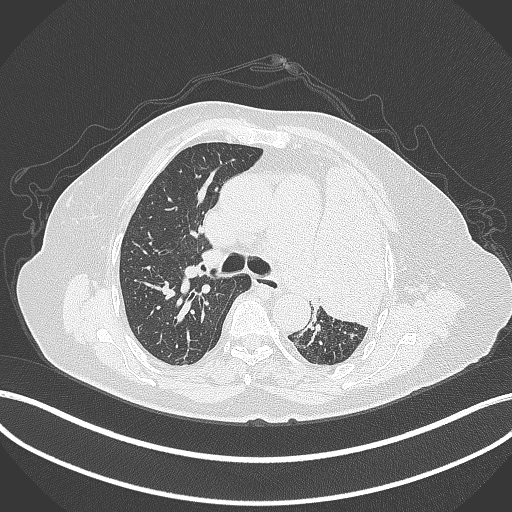
Chest CT, one axial slice. Position 251 of 399 along the scan axis. Reconstruction kernel B70f. 120 kVp. Lung window (W 1500 / L -600 HU). 1 mm slice thickness. 512 × 512 image matrix, field of view 400 × 400 mm. Patient: female, 75 years. Case-level facts recorded for this patient, not image findings: clinical TNM (as recorded): T3 N3 M1.
Structures marked on this image (bounding box drawn by a radiologist):
- lung tumour (recorded histology: adenocarcinoma): bounding box [x1, y1, x2, y2] px = [305, 156, 398, 332]